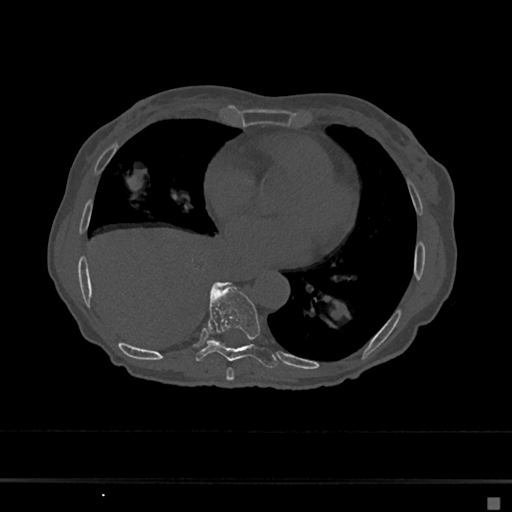
CT including the spine, one axial slice. Slice 321 of 797 in the series (ordered by position). Reconstruction kernel Br40s/3. 120 kVp. Bone window (W 1800 / L 400 HU). 0.5 mm slice thickness. 512 × 512 image matrix. Patient: female, 68 years. Case-level facts recorded for this patient, not image findings: primary cancer: renal.
Annotated regions visible in this slice (semi-automatic segmentation, software-assisted and operator-edited):
- T7 vertebra: bounding box [x1, y1, x2, y2] px = [226, 367, 234, 381]
- T8 vertebra: [195, 282, 278, 368]
- T9 vertebra: [216, 282, 224, 287]